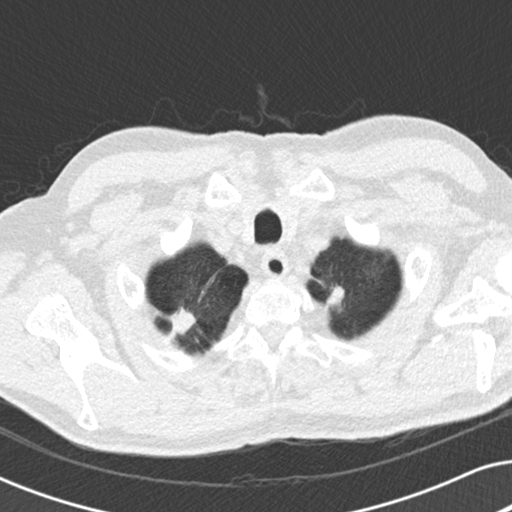
Low-dose screening chest CT, one axial slice; slice 174 of 191 in the series (ordered by position); reconstruction kernel B30f; 120 kVp; lung window (W 1500 / L -600 HU); 2 mm slice thickness; 512 × 512 image matrix, field of view 330 × 330 mm.
Structures marked on this image (expert manual segmentation):
- lesion 2 (nodule, lower lobe of right lung): bounding box <169,308,196,335> (left, top, right, bottom; pixels)